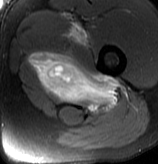
MRI of an extremity soft-tissue mass, one axial slice. Slice 63 of 70 in the series (ordered by position). T2-weighted fat-saturated. MR volume resampled by the dataset authors to the PET/CT grid (not the native acquisition matrix). 3.27 mm slice thickness. 158 × 164 image matrix, field of view 154 × 160 mm. Male patient. Case-level facts recorded for this patient, not image findings: histological type: extraskeletal osteosarcoma; grade: high; site of the primary tumour: left adductur.
Outlined on this slice (expert contour drawn on MRI and transferred to this co-registered scan by the dataset authors):
- gross tumour volume (mass): bounding box [x1, y1, x2, y2] px = [29, 22, 123, 113]